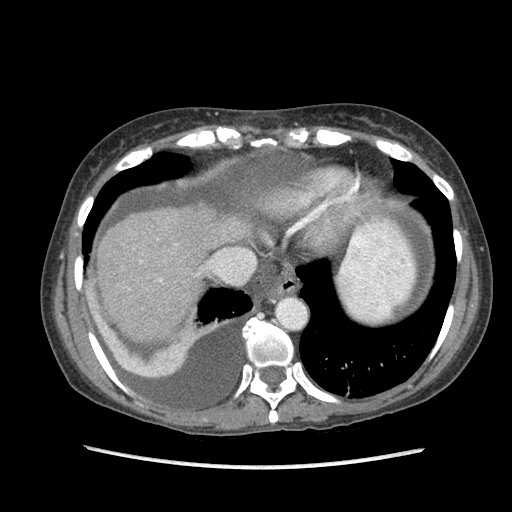
Contrast-enhanced abdominal CT (liver protocol), one axial slice. Reconstruction kernel STANDARD. 120 kVp. Soft-tissue window (W 400 / L 40 HU). 512 × 512 image matrix. From the clinical record (not read from this slice): diagnosis: hepatocellular carcinoma (patient treated with transarterial chemoembolisation; whether this scan precedes or follows treatment is not stated here); TNM stage (as recorded): Stage-IIIB; Child-Pugh class: A; tumour differentiation: no biopsy; tumour nodularity: uninodular.
Annotated regions visible in this slice (semi-automatically segmented with operator editing):
- liver parenchyma outside the tumour (the mass and vessels are separate outlines, so this box may not span the whole liver): bounding box <96,204,249,336> (left, top, right, bottom; pixels)